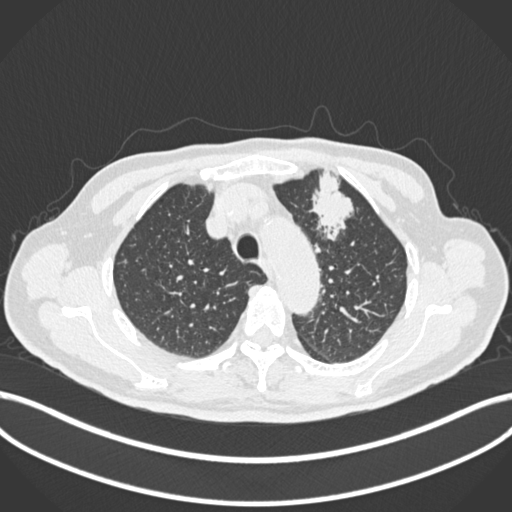
Chest CT, one axial slice. Position 200 of 261 along the scan axis. 120 kVp. Lung window (W 1500 / L -600 HU). 1 mm slice thickness. 512 × 512 image matrix, field of view 400 × 400 mm. Patient: male, 74 years. From the clinical record (not read from this slice): clinical TNM (as recorded): T2b N0 M1c.
Annotated regions visible in this slice (rectangle marked by the reading radiologist):
- lung tumour (recorded histology: adenocarcinoma): bounding box <312,168,362,241> (left, top, right, bottom; pixels)